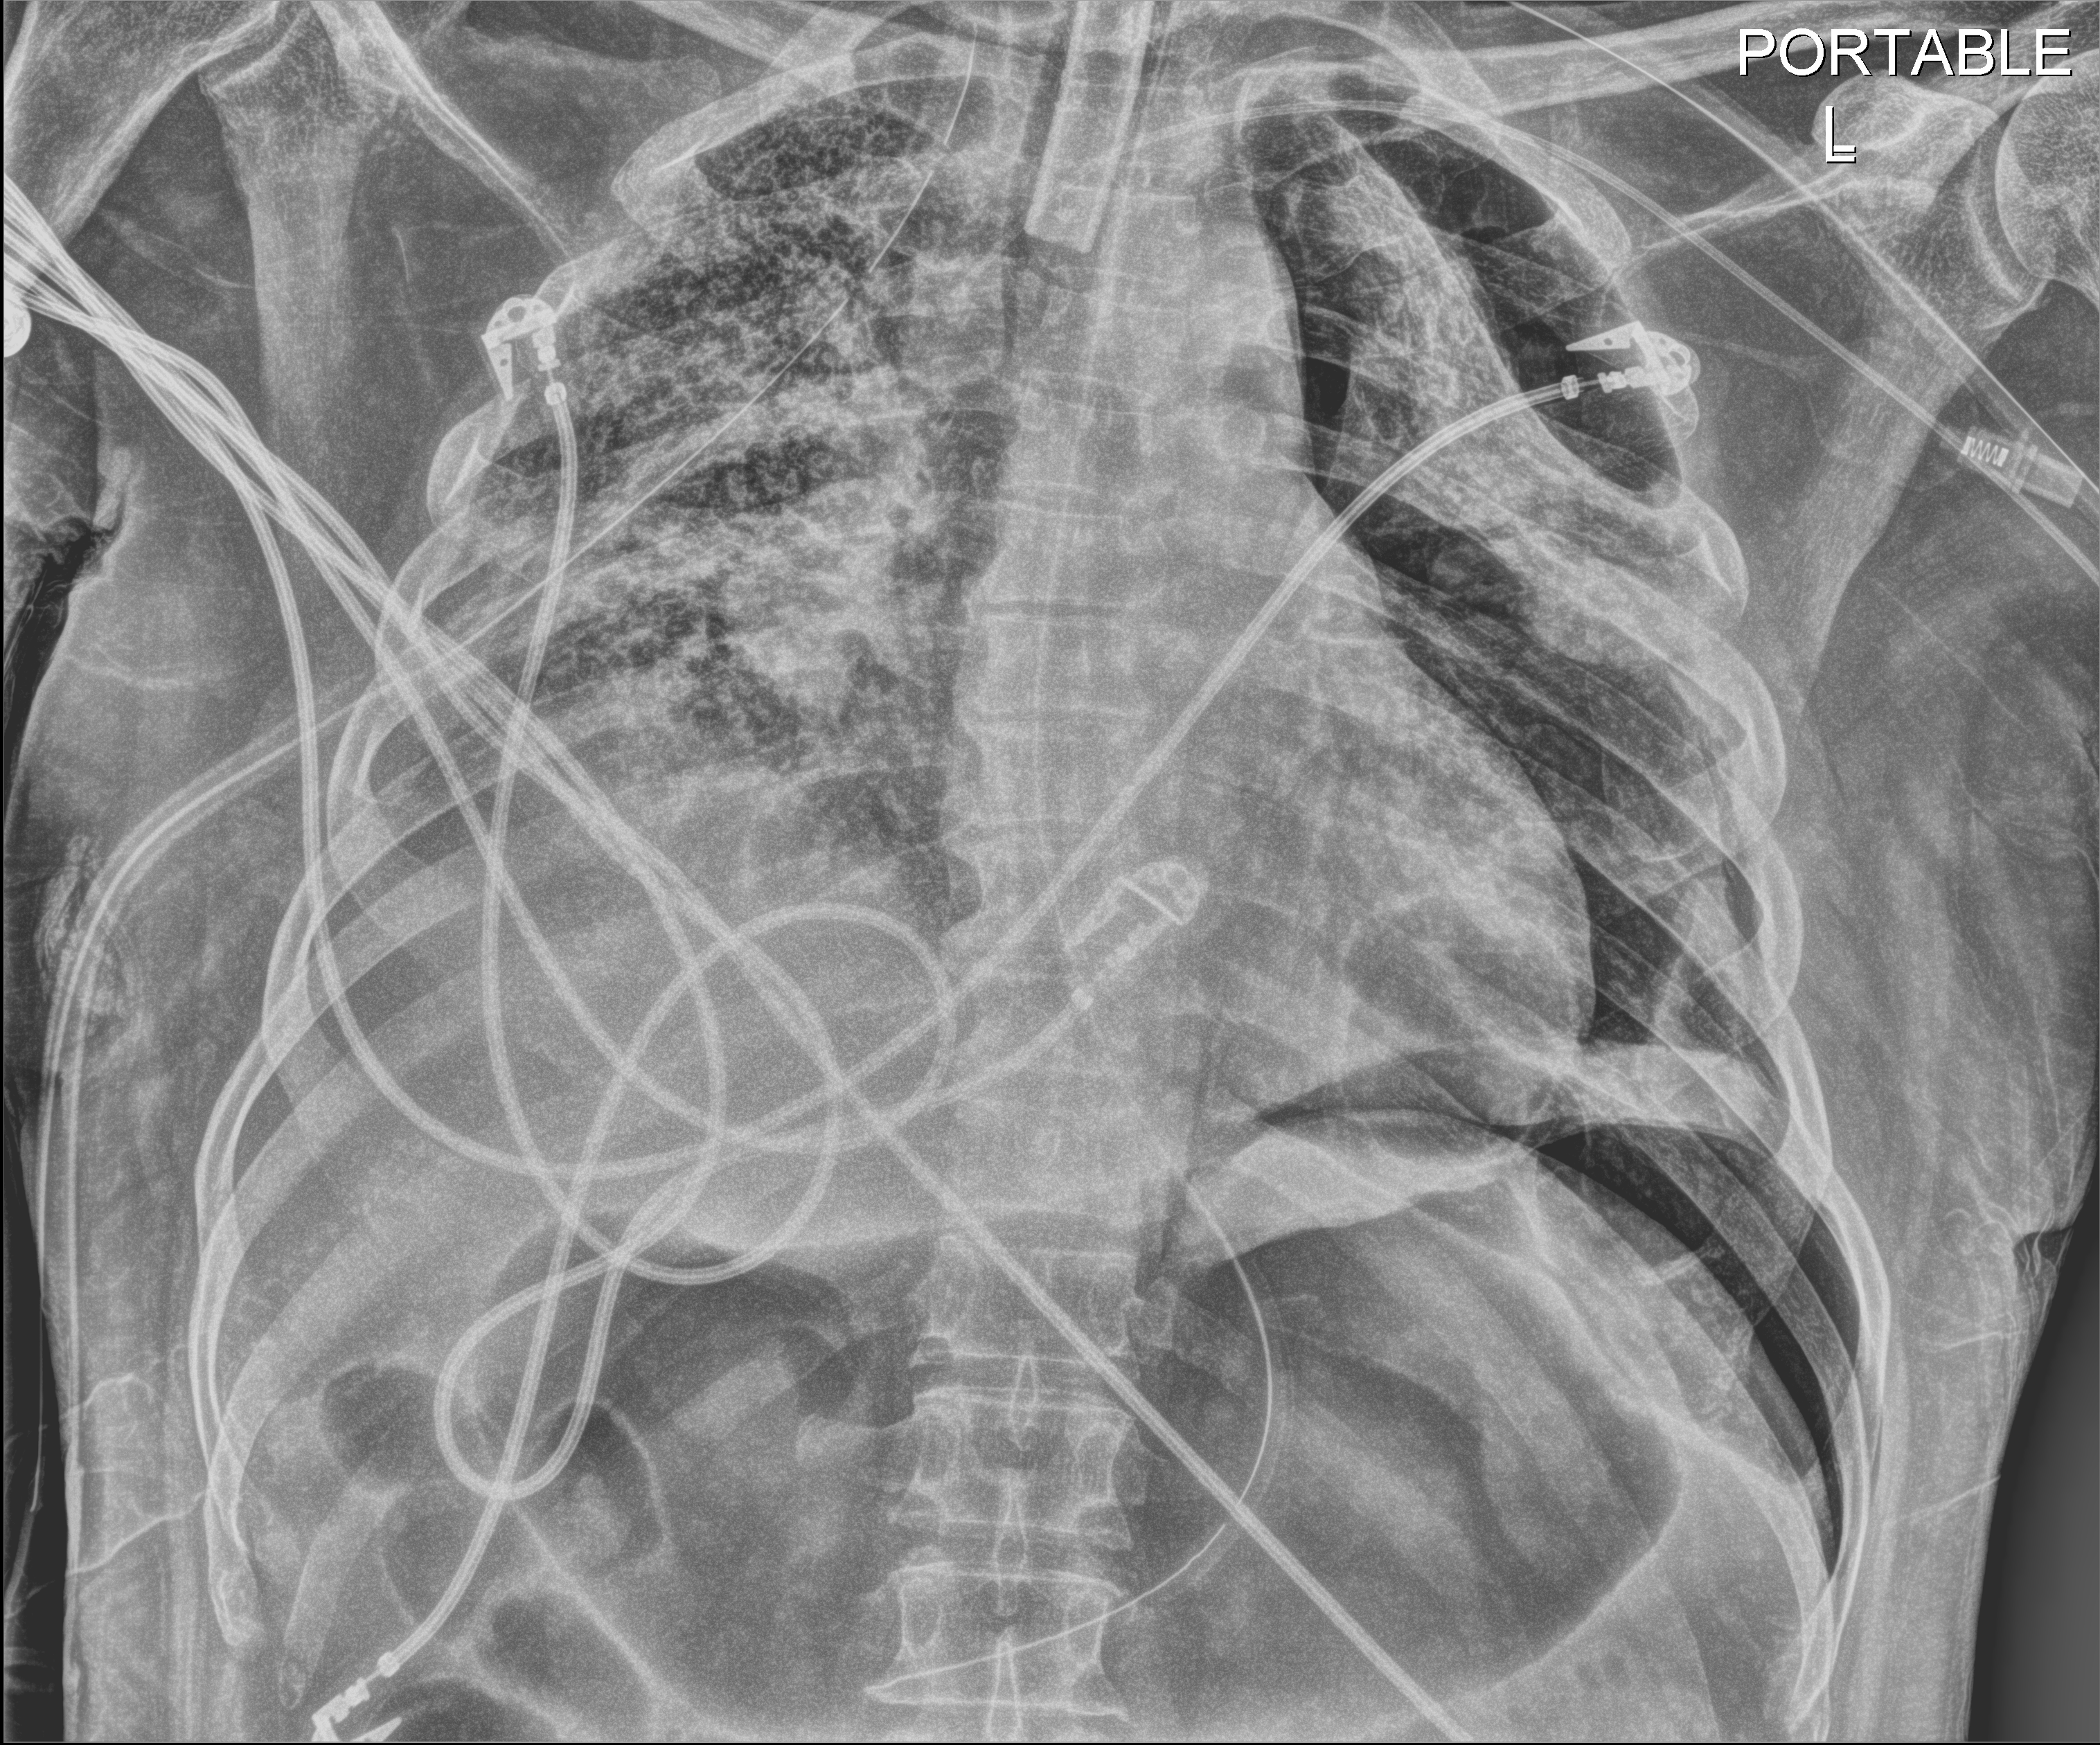
Chest X-ray (portable); anteroposterior (AP) projection. Patient hospitalised with COVID-19; male, aged 18–59 years.
Admission-level facts for this patient (not findings on this image; timing relative to this image not recorded):
- length of hospital stay: 83 days
- mechanically ventilated during this hospital stay: yes
- admitted to intensive care during this hospital stay: yes